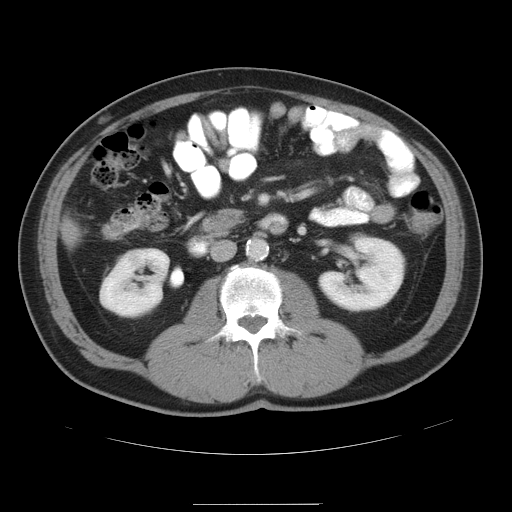
Contrast-enhanced abdominal CT, one axial slice. Slice 15 of 47 in the series (ordered by position). 120 kVp. Soft-tissue window (W 400 / L 40 HU). 5 mm slice thickness. 512 × 512 image matrix, field of view 420 × 420 mm. Male patient, age 61 years. From the clinical record (not read from this slice): diagnosis: colorectal cancer liver metastases, imaged before liver resection; multiple liver metastases: no; largest metastasis: 1.2 cm; disease in both lobes: no.
Annotated regions visible in this slice (manually delineated by an expert):
- liver: bounding box [x1, y1, x2, y2] px = [68, 225, 72, 239]